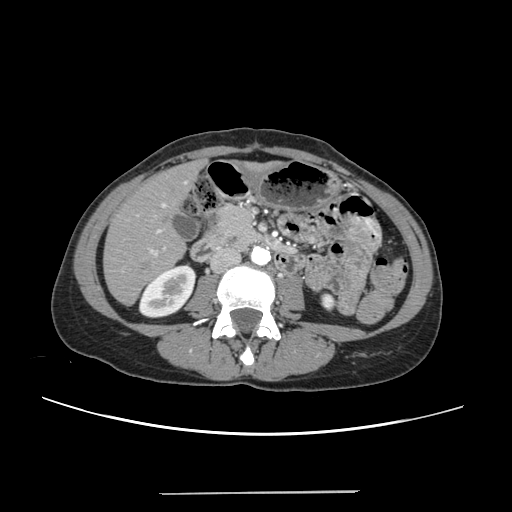
Contrast-enhanced abdominal CT, one axial slice. Position 81 of 240 along the scan axis. Intravenous contrast given. Soft-tissue window (W 400 / L 40 HU). 1.25 mm slice thickness. 512 × 512 image matrix, field of view 371 × 371 mm. Female patient, age 60 years. Case-level facts recorded for this patient, not image findings: diagnosis: colorectal cancer liver metastases, imaged before liver resection.
Structures marked on this image (manually delineated by an expert):
- liver: box from (x=105, y=163) to (x=199, y=304) px
- planned liver remnant (the part of the liver to remain after resection): (x=105, y=172)–(x=185, y=304)
- portal vein (with intrahepatic branches): (x=122, y=203)–(x=166, y=271)